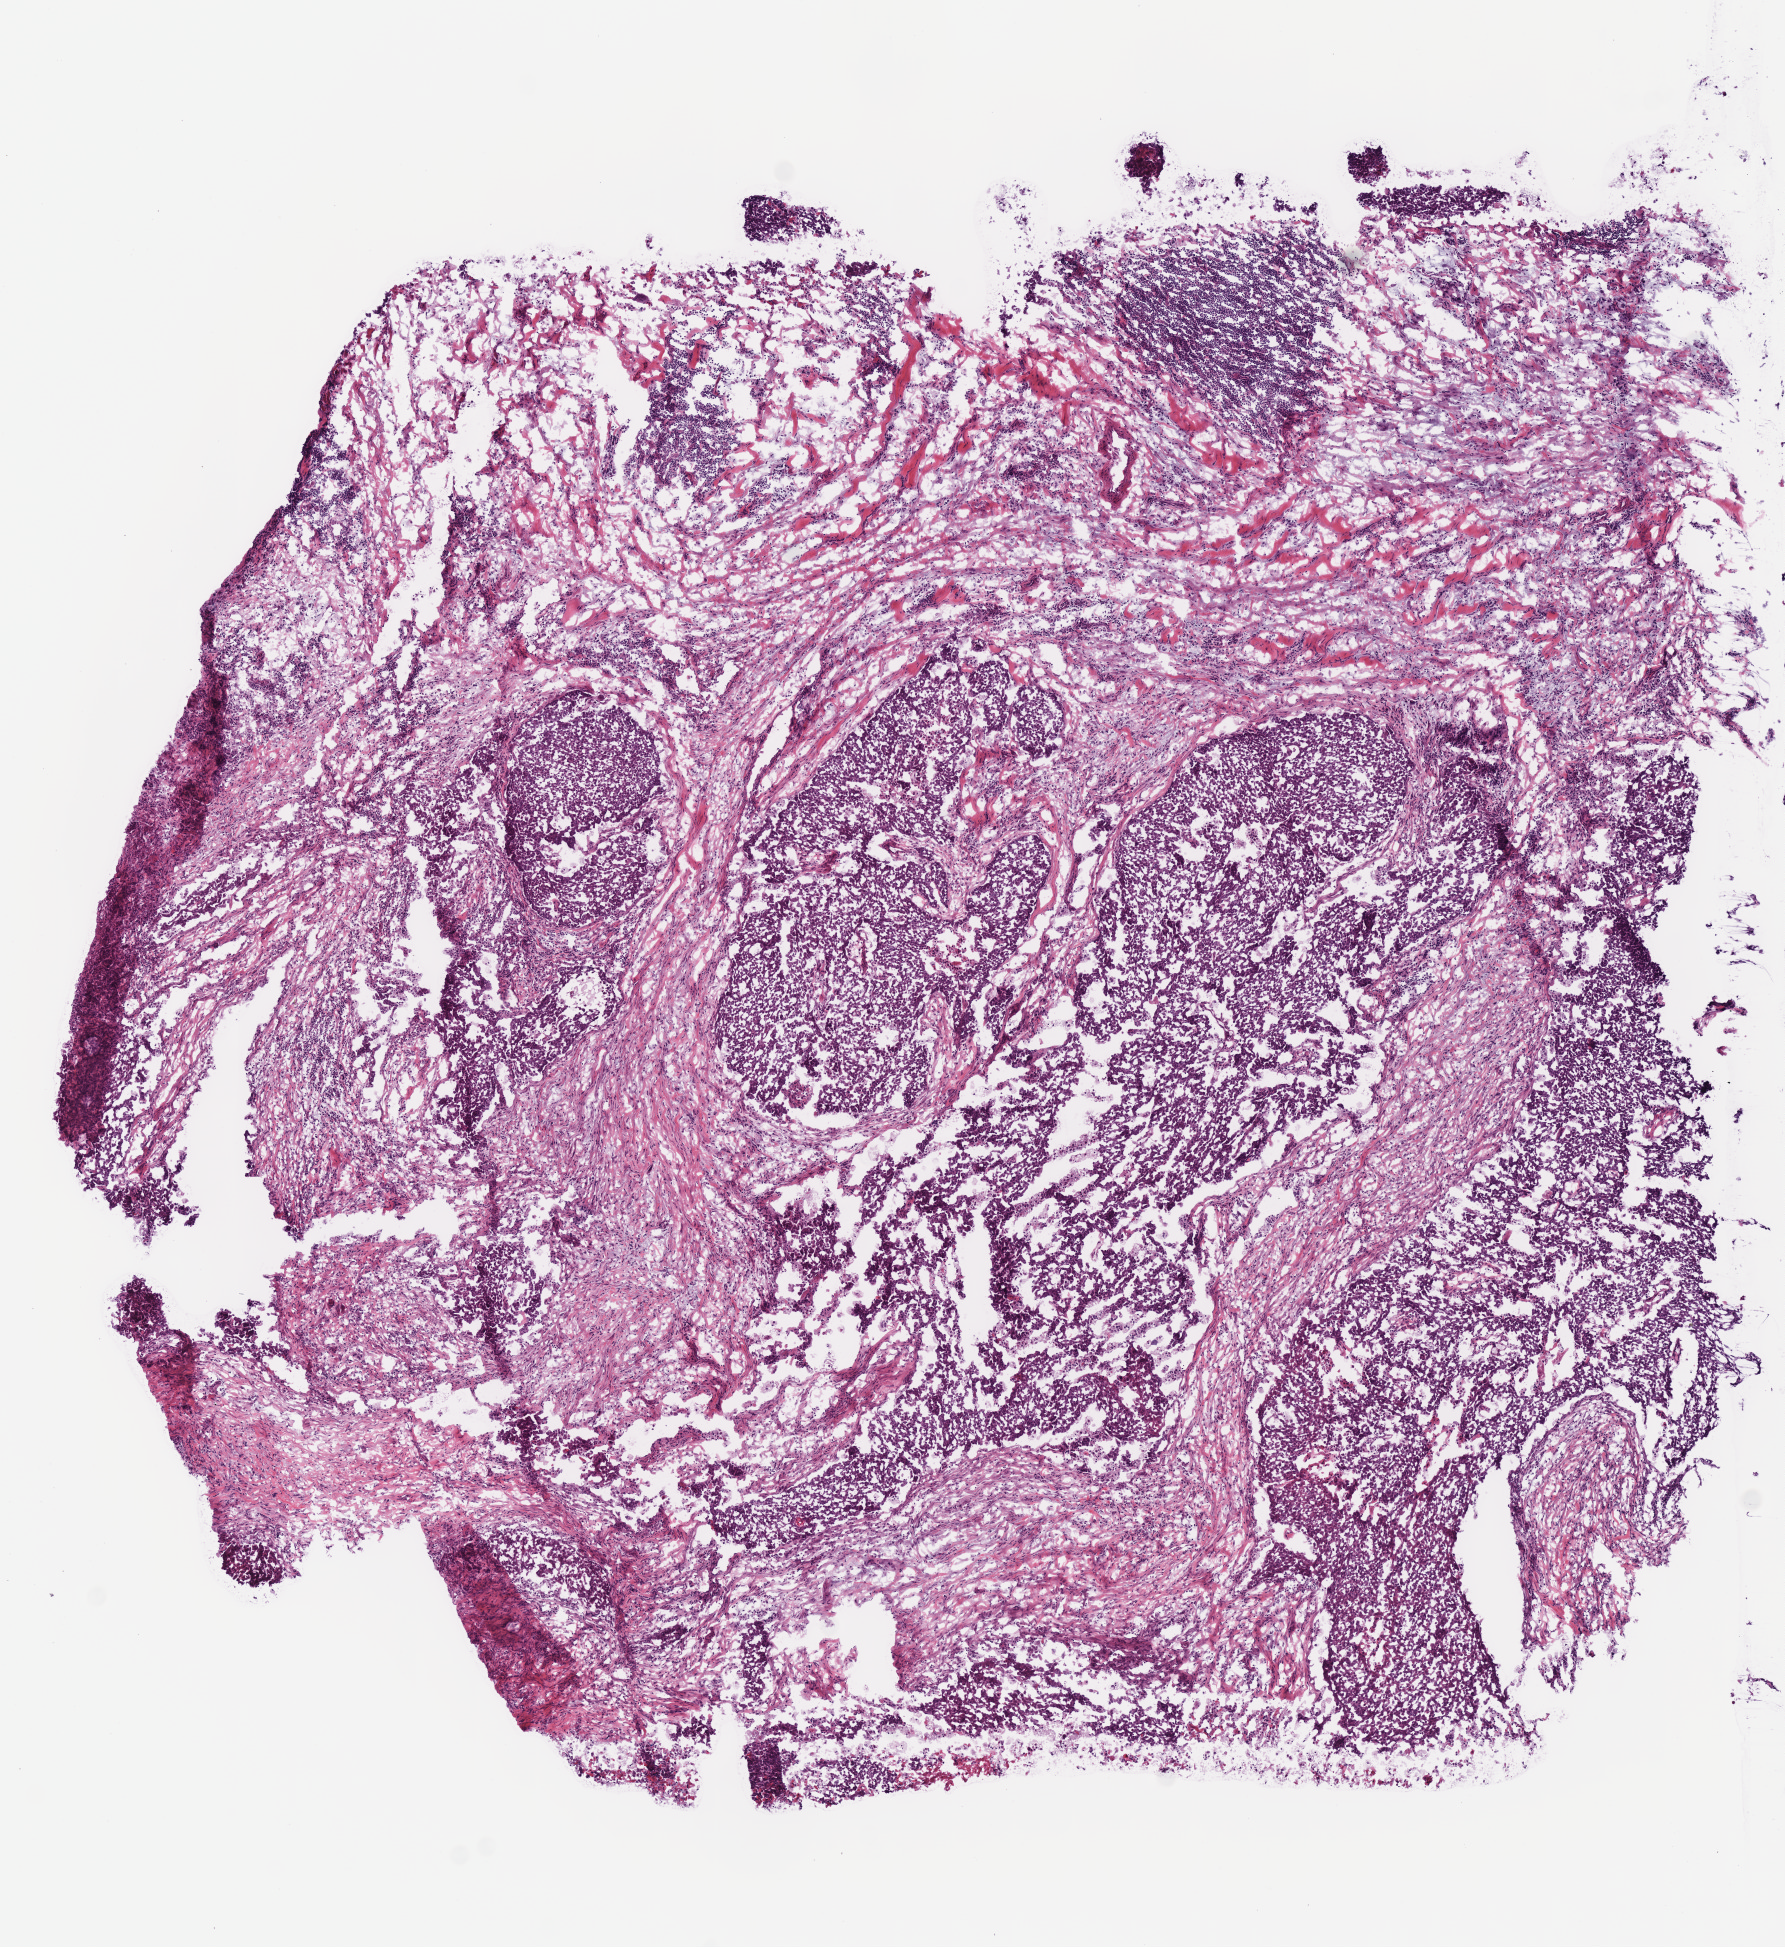
Whole-slide histology image, H&E — shown as a low-resolution overview of the whole scanned area (about 7.0 x 7.7 mm); frozen section; sample: primary tumour, head and neck. Patient: male, age at initial diagnosis 62 years. Histologic grade: G2 (moderately differentiated). Composition of this section per pathologist review: tumour cells 60%, tumour nuclei 50%, normal cells 0%, stromal cells 40%, necrosis 0%. Infiltration values recorded for this section: lymphocyte infiltration 35%, monocyte infiltration 0%, neutrophil infiltration 0%.
• lymph nodes positive (case pathology): 2 of 28 examined
• histologic diagnosis: Squamous cell carcinoma, NOS (larynx, NOS)
• AJCC pathologic stage: IVA (7th edition)